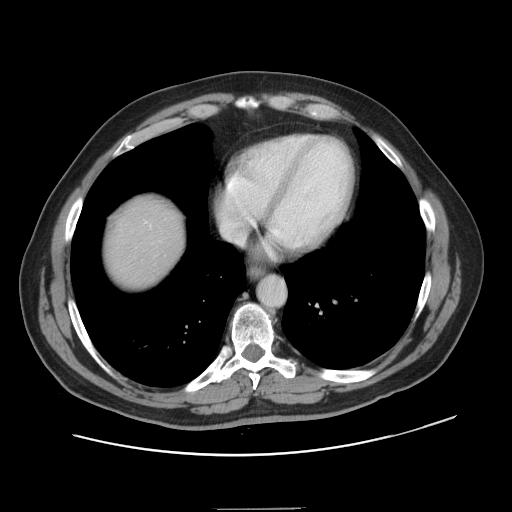
Contrast-enhanced abdominal CT, one axial slice. Position 138 of 143 along the scan axis. 120 kVp. Intravenous contrast given. Soft-tissue window (W 400 / L 40 HU). 2.5 mm slice thickness. 512 × 512 image matrix, field of view 402 × 402 mm. Male patient, age 62 years. From the clinical record (not read from this slice): diagnosis: colorectal cancer liver metastases, imaged before liver resection.
Outlined on this slice (manually delineated by an expert):
- liver: bounding box [x1, y1, x2, y2] px = [107, 202, 183, 287]
- planned liver remnant (the part of the liver to remain after resection): [107, 202, 183, 287]